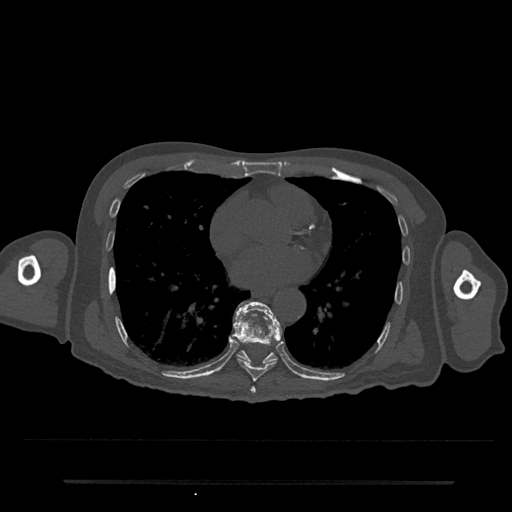
CT including the spine, one axial slice; position 402 of 797 along the scan axis; reconstruction kernel Br40s/3; 120 kVp; bone window (W 1800 / L 400 HU); 0.5 mm slice thickness; 512 × 512 image matrix, field of view 427 × 427 mm. Patient: male, 74 years. Case-level facts recorded for this patient, not image findings: primary cancer: prostate.
Annotated regions visible in this slice (semi-automatically segmented with operator editing):
- T7 vertebra: bounding box <250,386,256,394> (left, top, right, bottom; pixels)
- T8 vertebra: <233,301,282,382>
- T9 vertebra: <235,303,282,364>